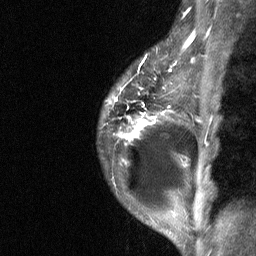
Breast MRI (dynamic contrast-enhanced), one sagittal slice. Slice 51 of 64 in the series (ordered by position). Dynamic contrast-enhanced study with each time point stored as its own series, time point 2 of 3 at this slice position (early post-contrast, ordered by acquisition time). 1.5 T. TE 4.8 ms, TR 27 ms. 256 × 256 image matrix, field of view 180 × 180 mm. Patient: female, 34 years. Case-level facts recorded for this patient, not image findings: setting: breast cancer imaged before/during neoadjuvant chemotherapy; receptor status: HR-positive, HER2-negative.
Structures marked on this image (semi-automatic segmentation, software-assisted and operator-edited):
- analysis volume of interest (the breast-tissue region the enhancement analysis was run in; not a lesion): bounding box (x1, y1, x2, y2) in pixels: (98, 44, 181, 191)
- tumour enhancement mask (voxels above the 90 % enhancement threshold inside the analysis volume of interest): (118, 63, 175, 139)